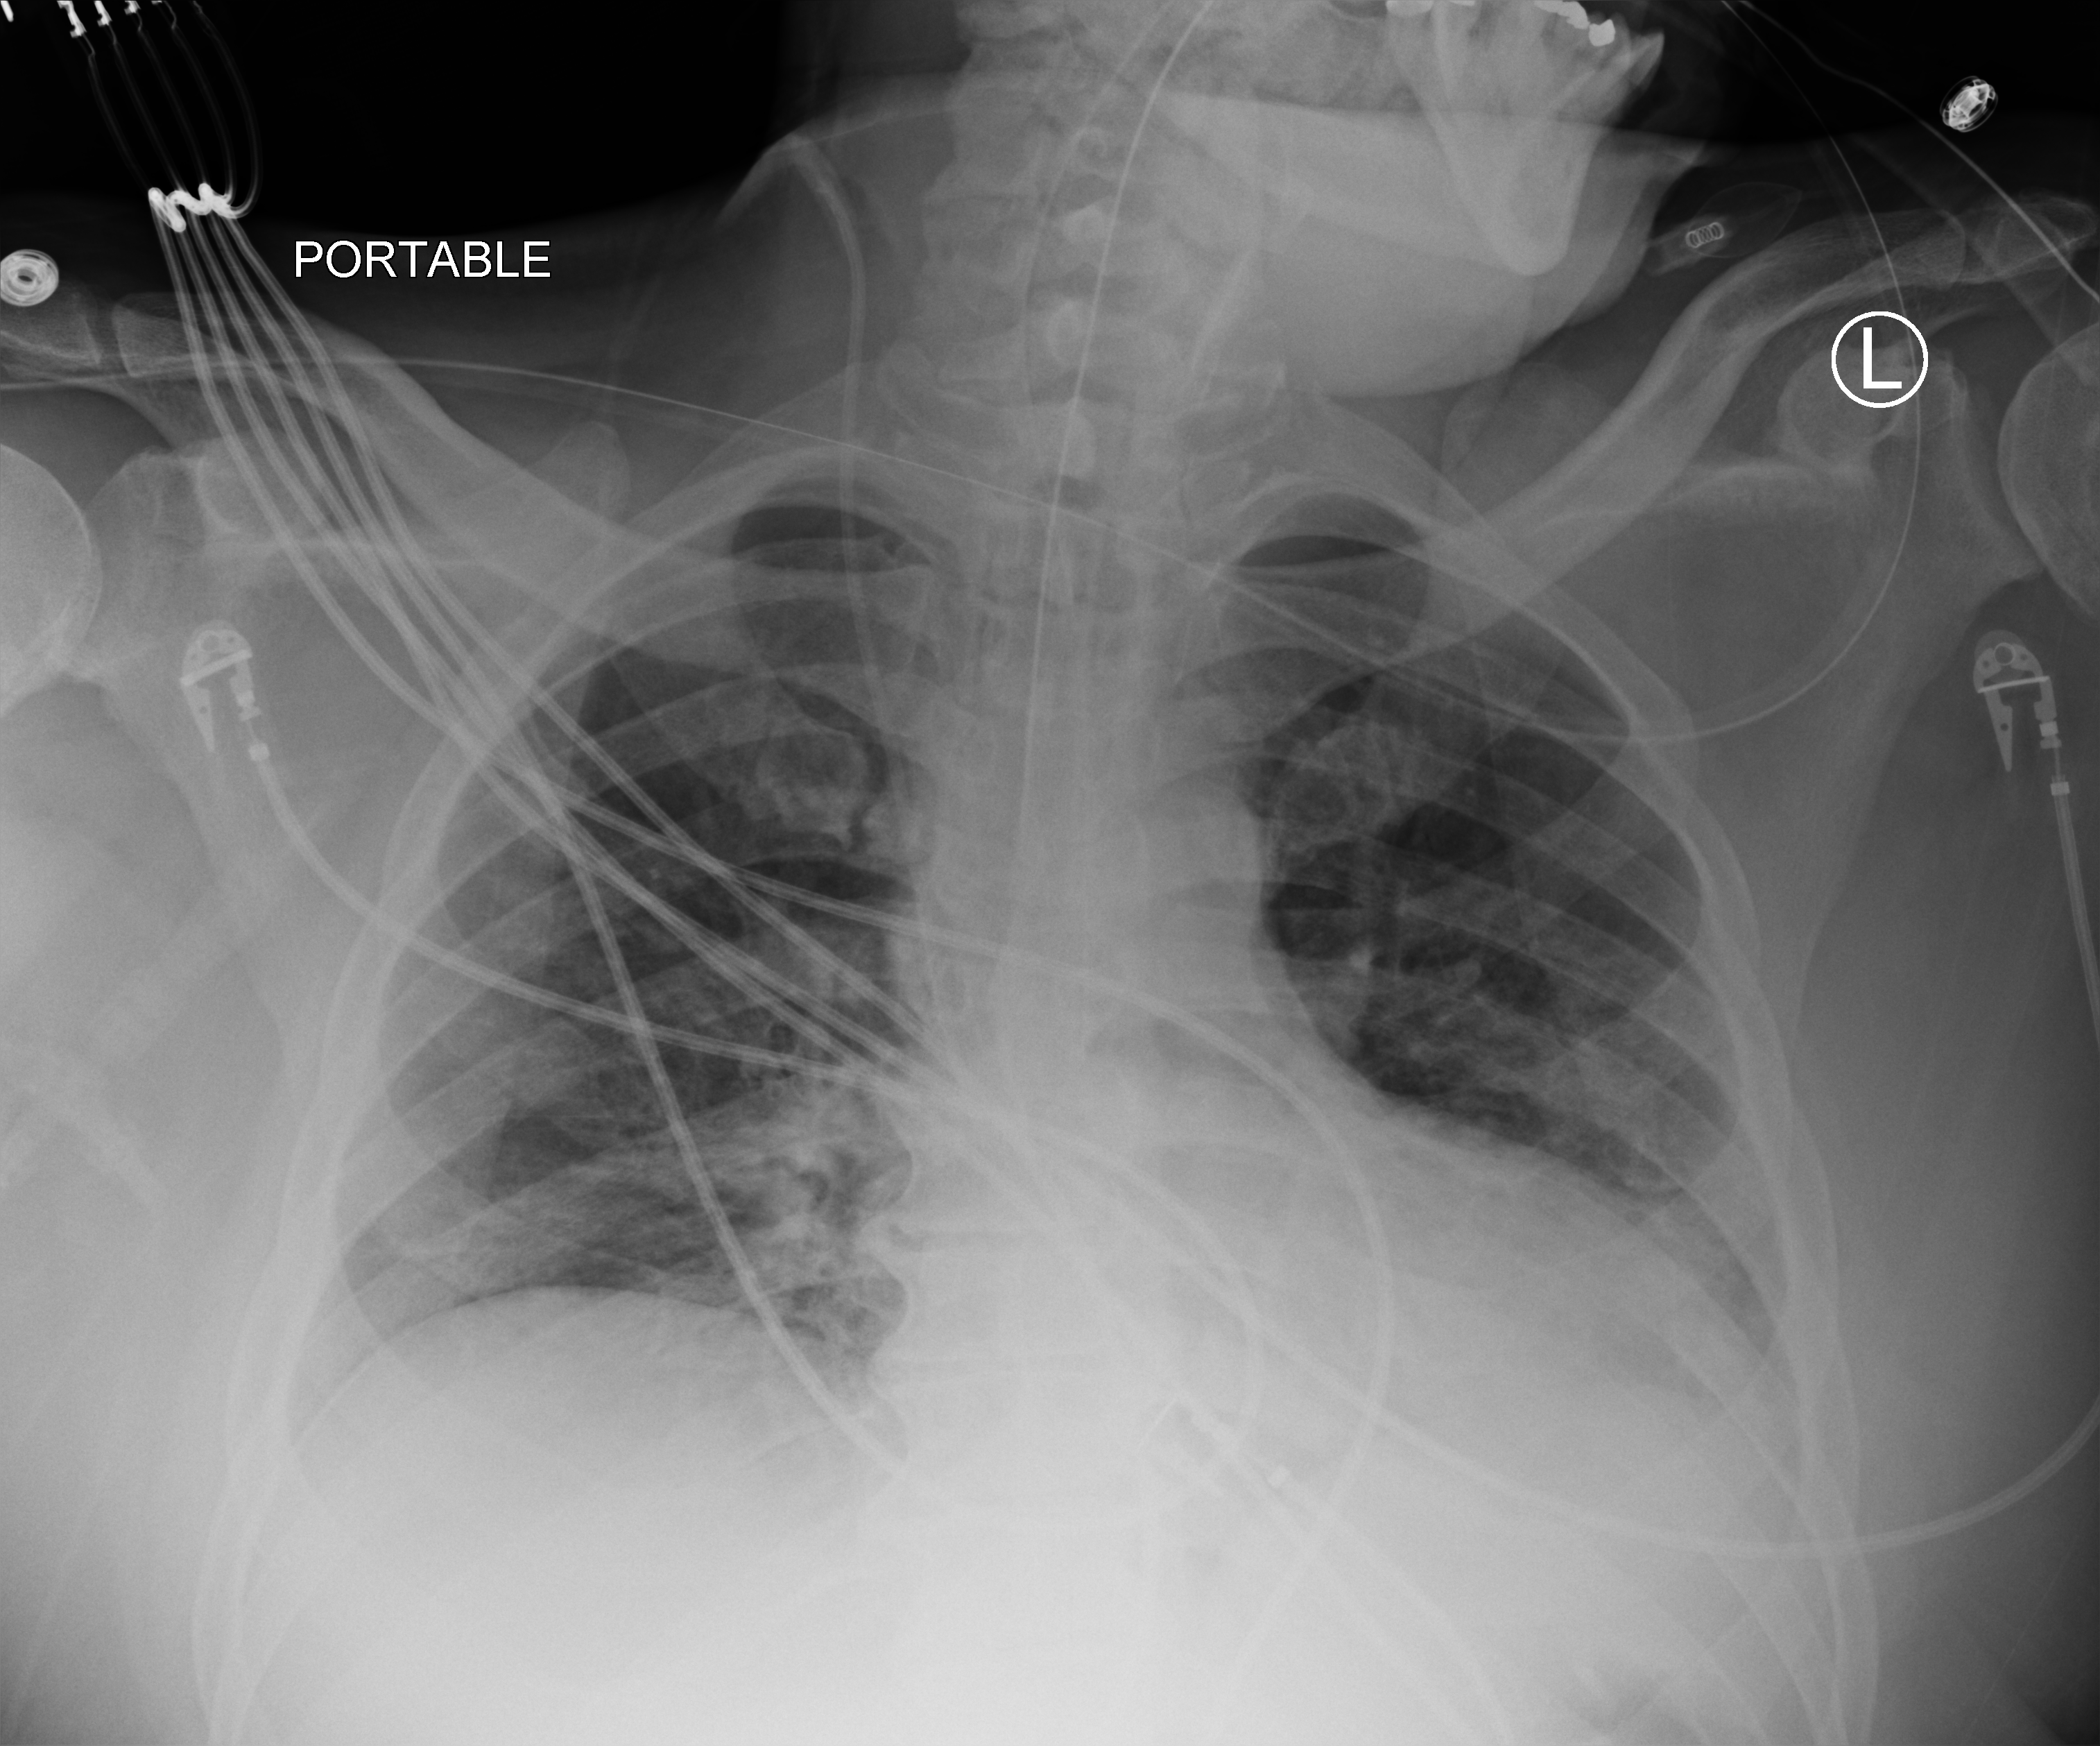
Bedside chest radiograph (computed radiography). Patient hospitalised with COVID-19; male, aged 18–59 years.
Admission-level facts for this patient (not findings on this image; timing relative to this image not recorded): mechanically ventilated during this hospital stay: yes; other chronic lung disease (admission record): no.